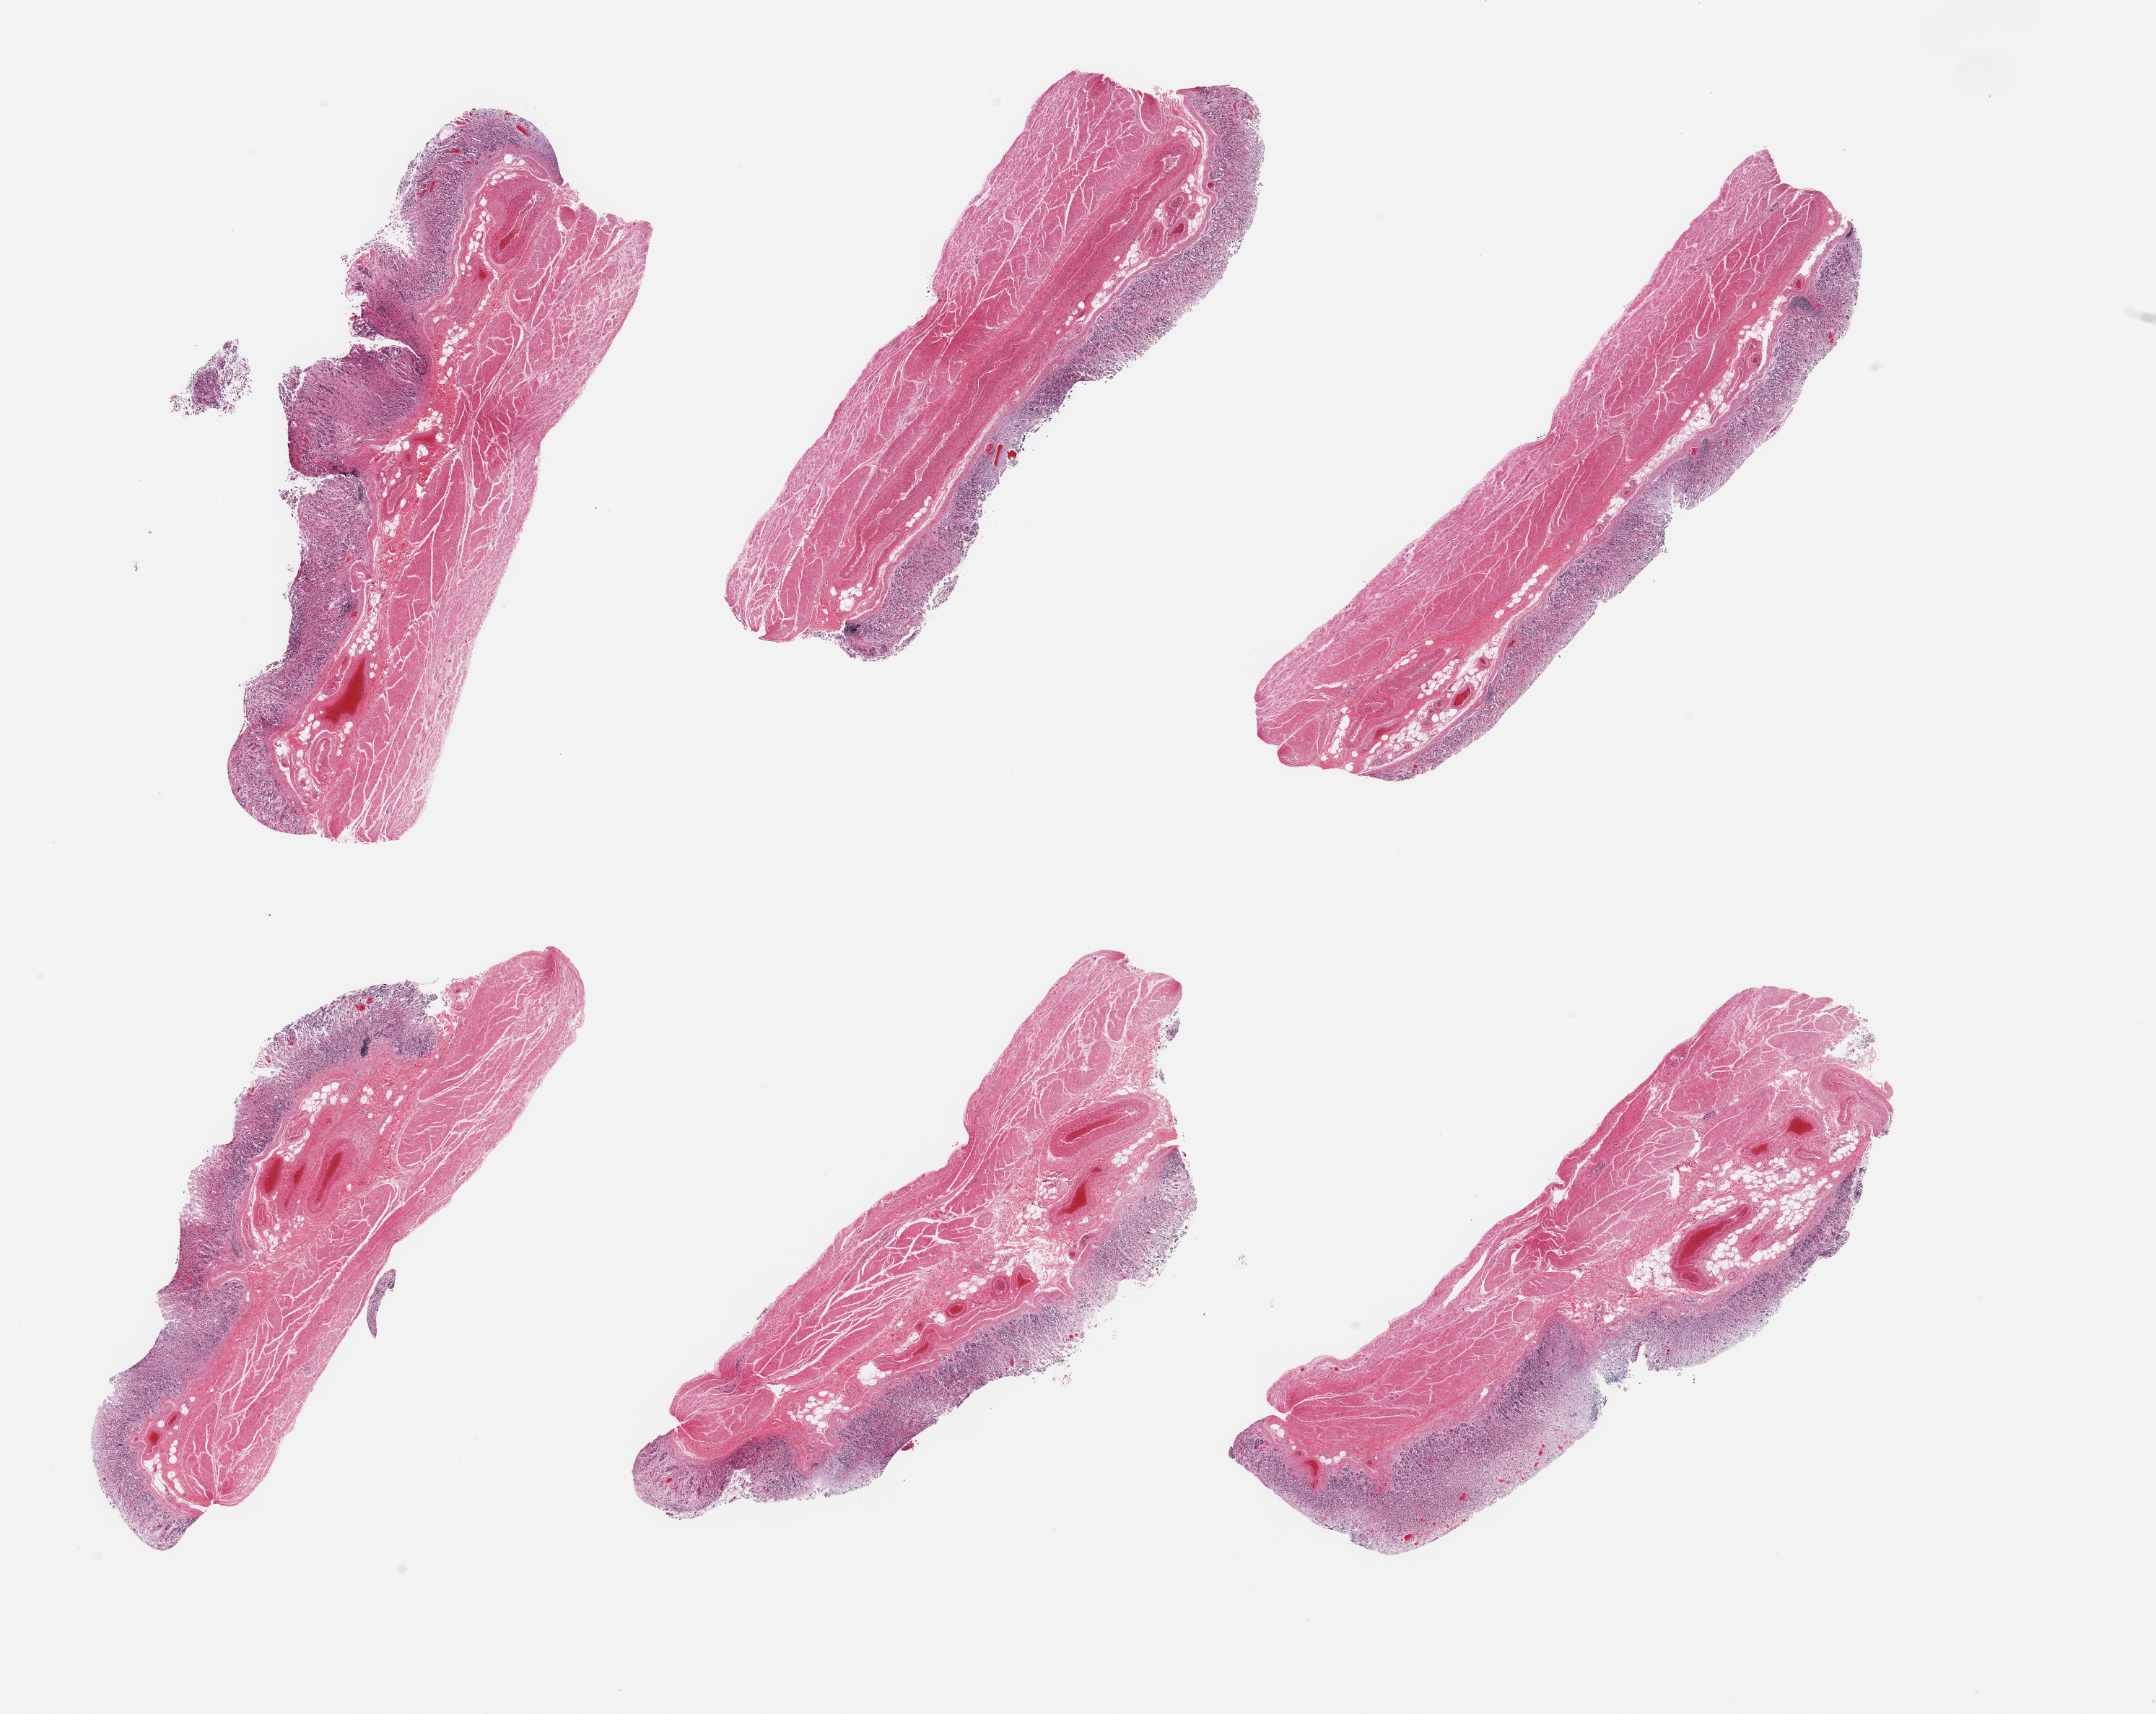
Whole-slide image, H&E stain, brightfield, whole scanned area (about 23.6 x 18.8 mm) shown as a low-resolution overview; PAXgene-fixed paraffin-embedded (PFPE) section; sampled site (target tissue): stomach; donor tissue sample. Donor sex: male.
Reviewer comment on this tissue sample: 6 pieces, mucosa up to ~0.6mm; glandular elements competely autolyzed.